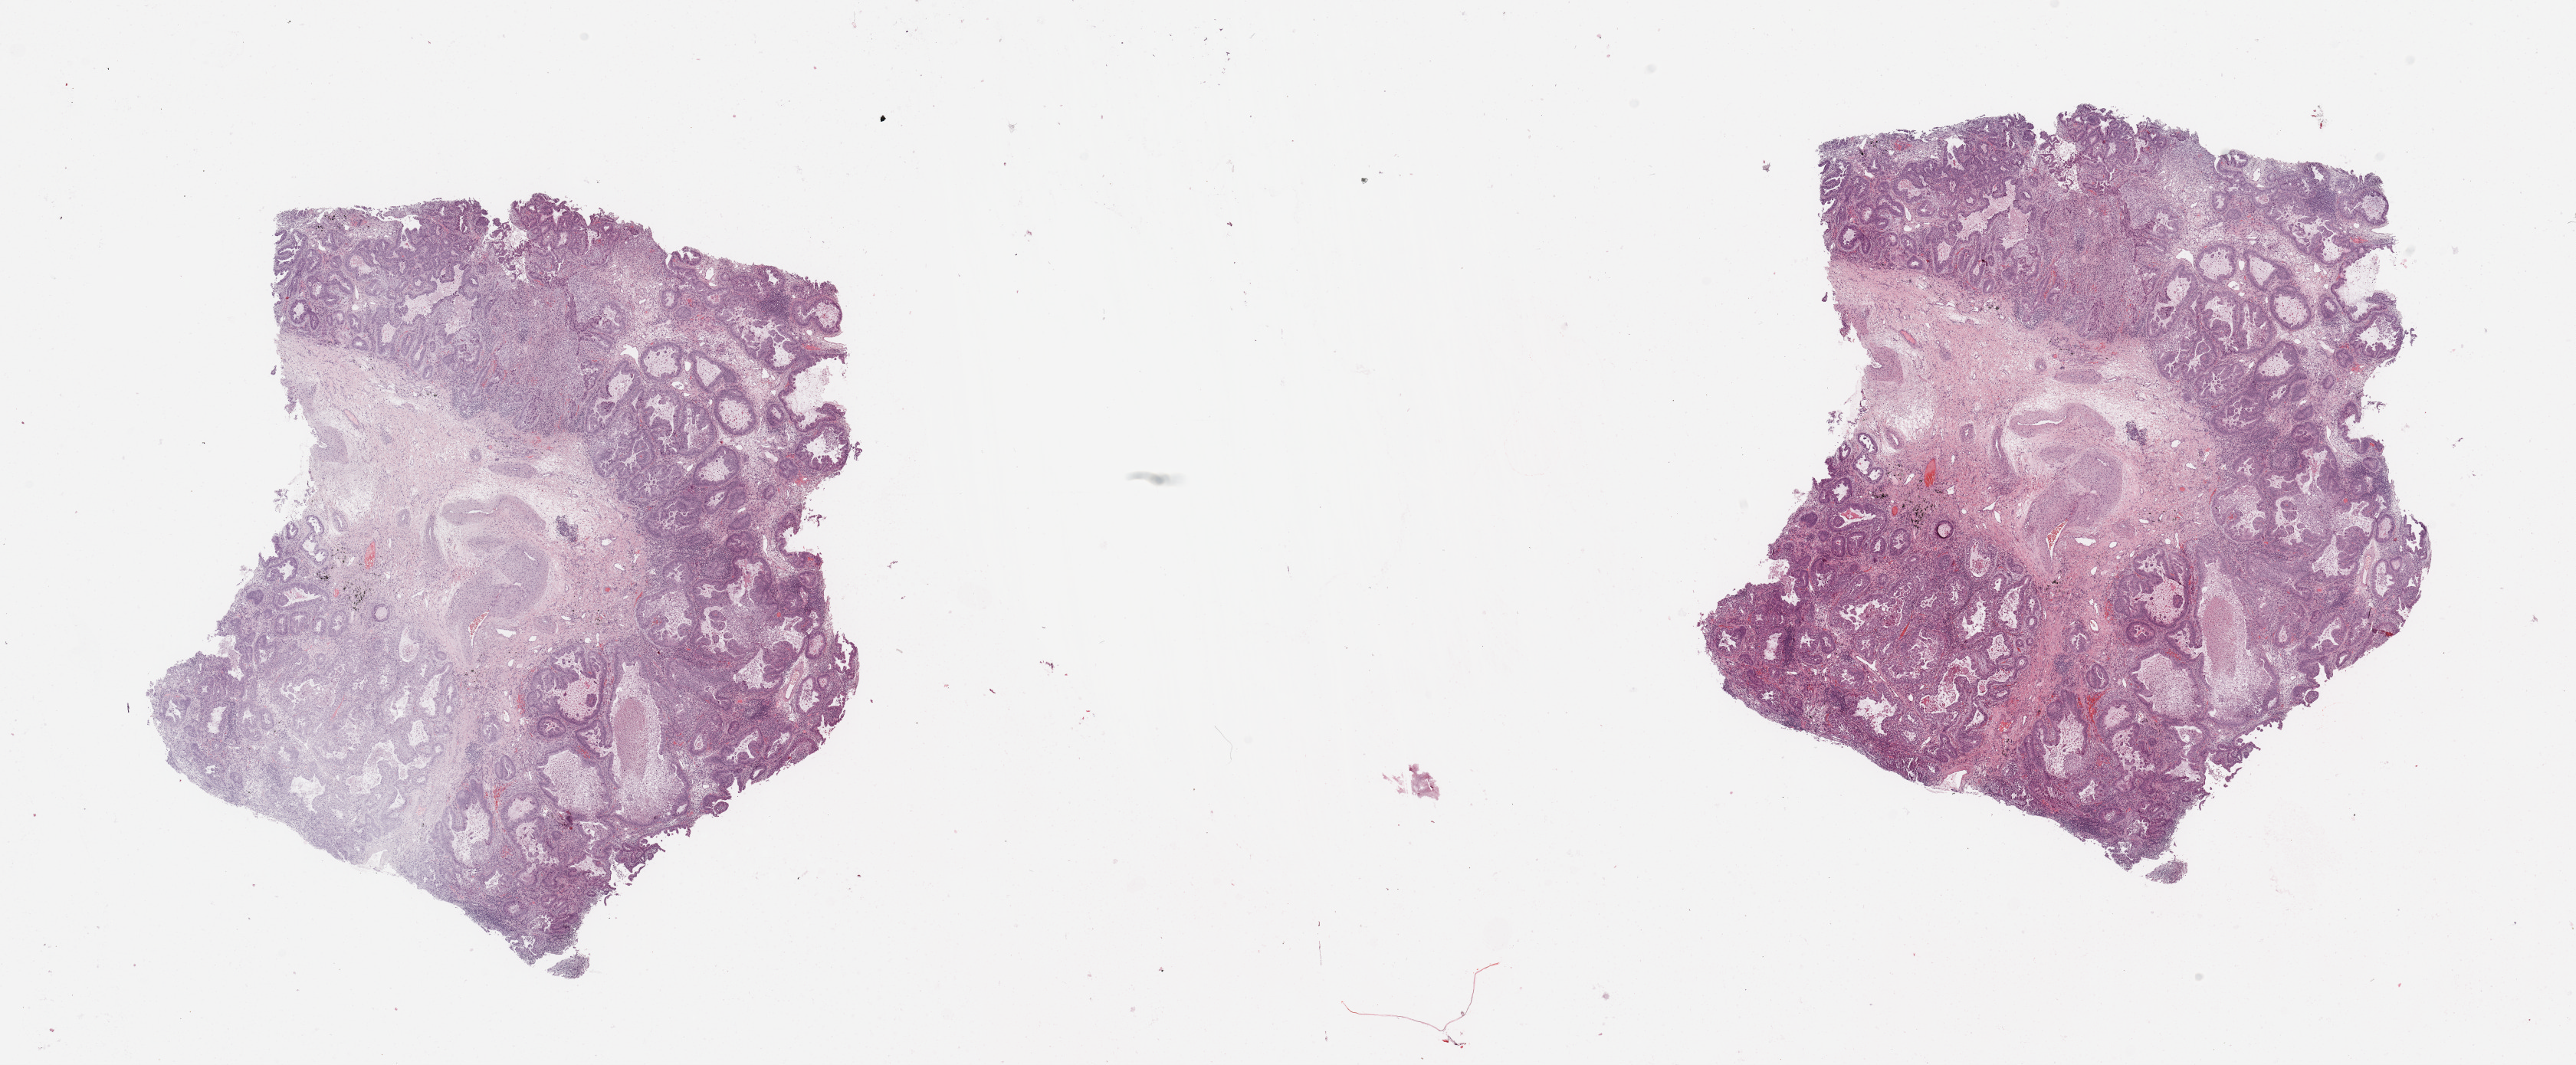
Whole-slide histology image, Hematoxylin and eosin (H&E) stained — low-resolution overview of the scanned area, about 26.6 x 11.0 mm (acquisition: 20x scan); lung, tissue type not recorded.
Patient diagnosis (cohort enrolment): lung adenocarcinoma (lung).